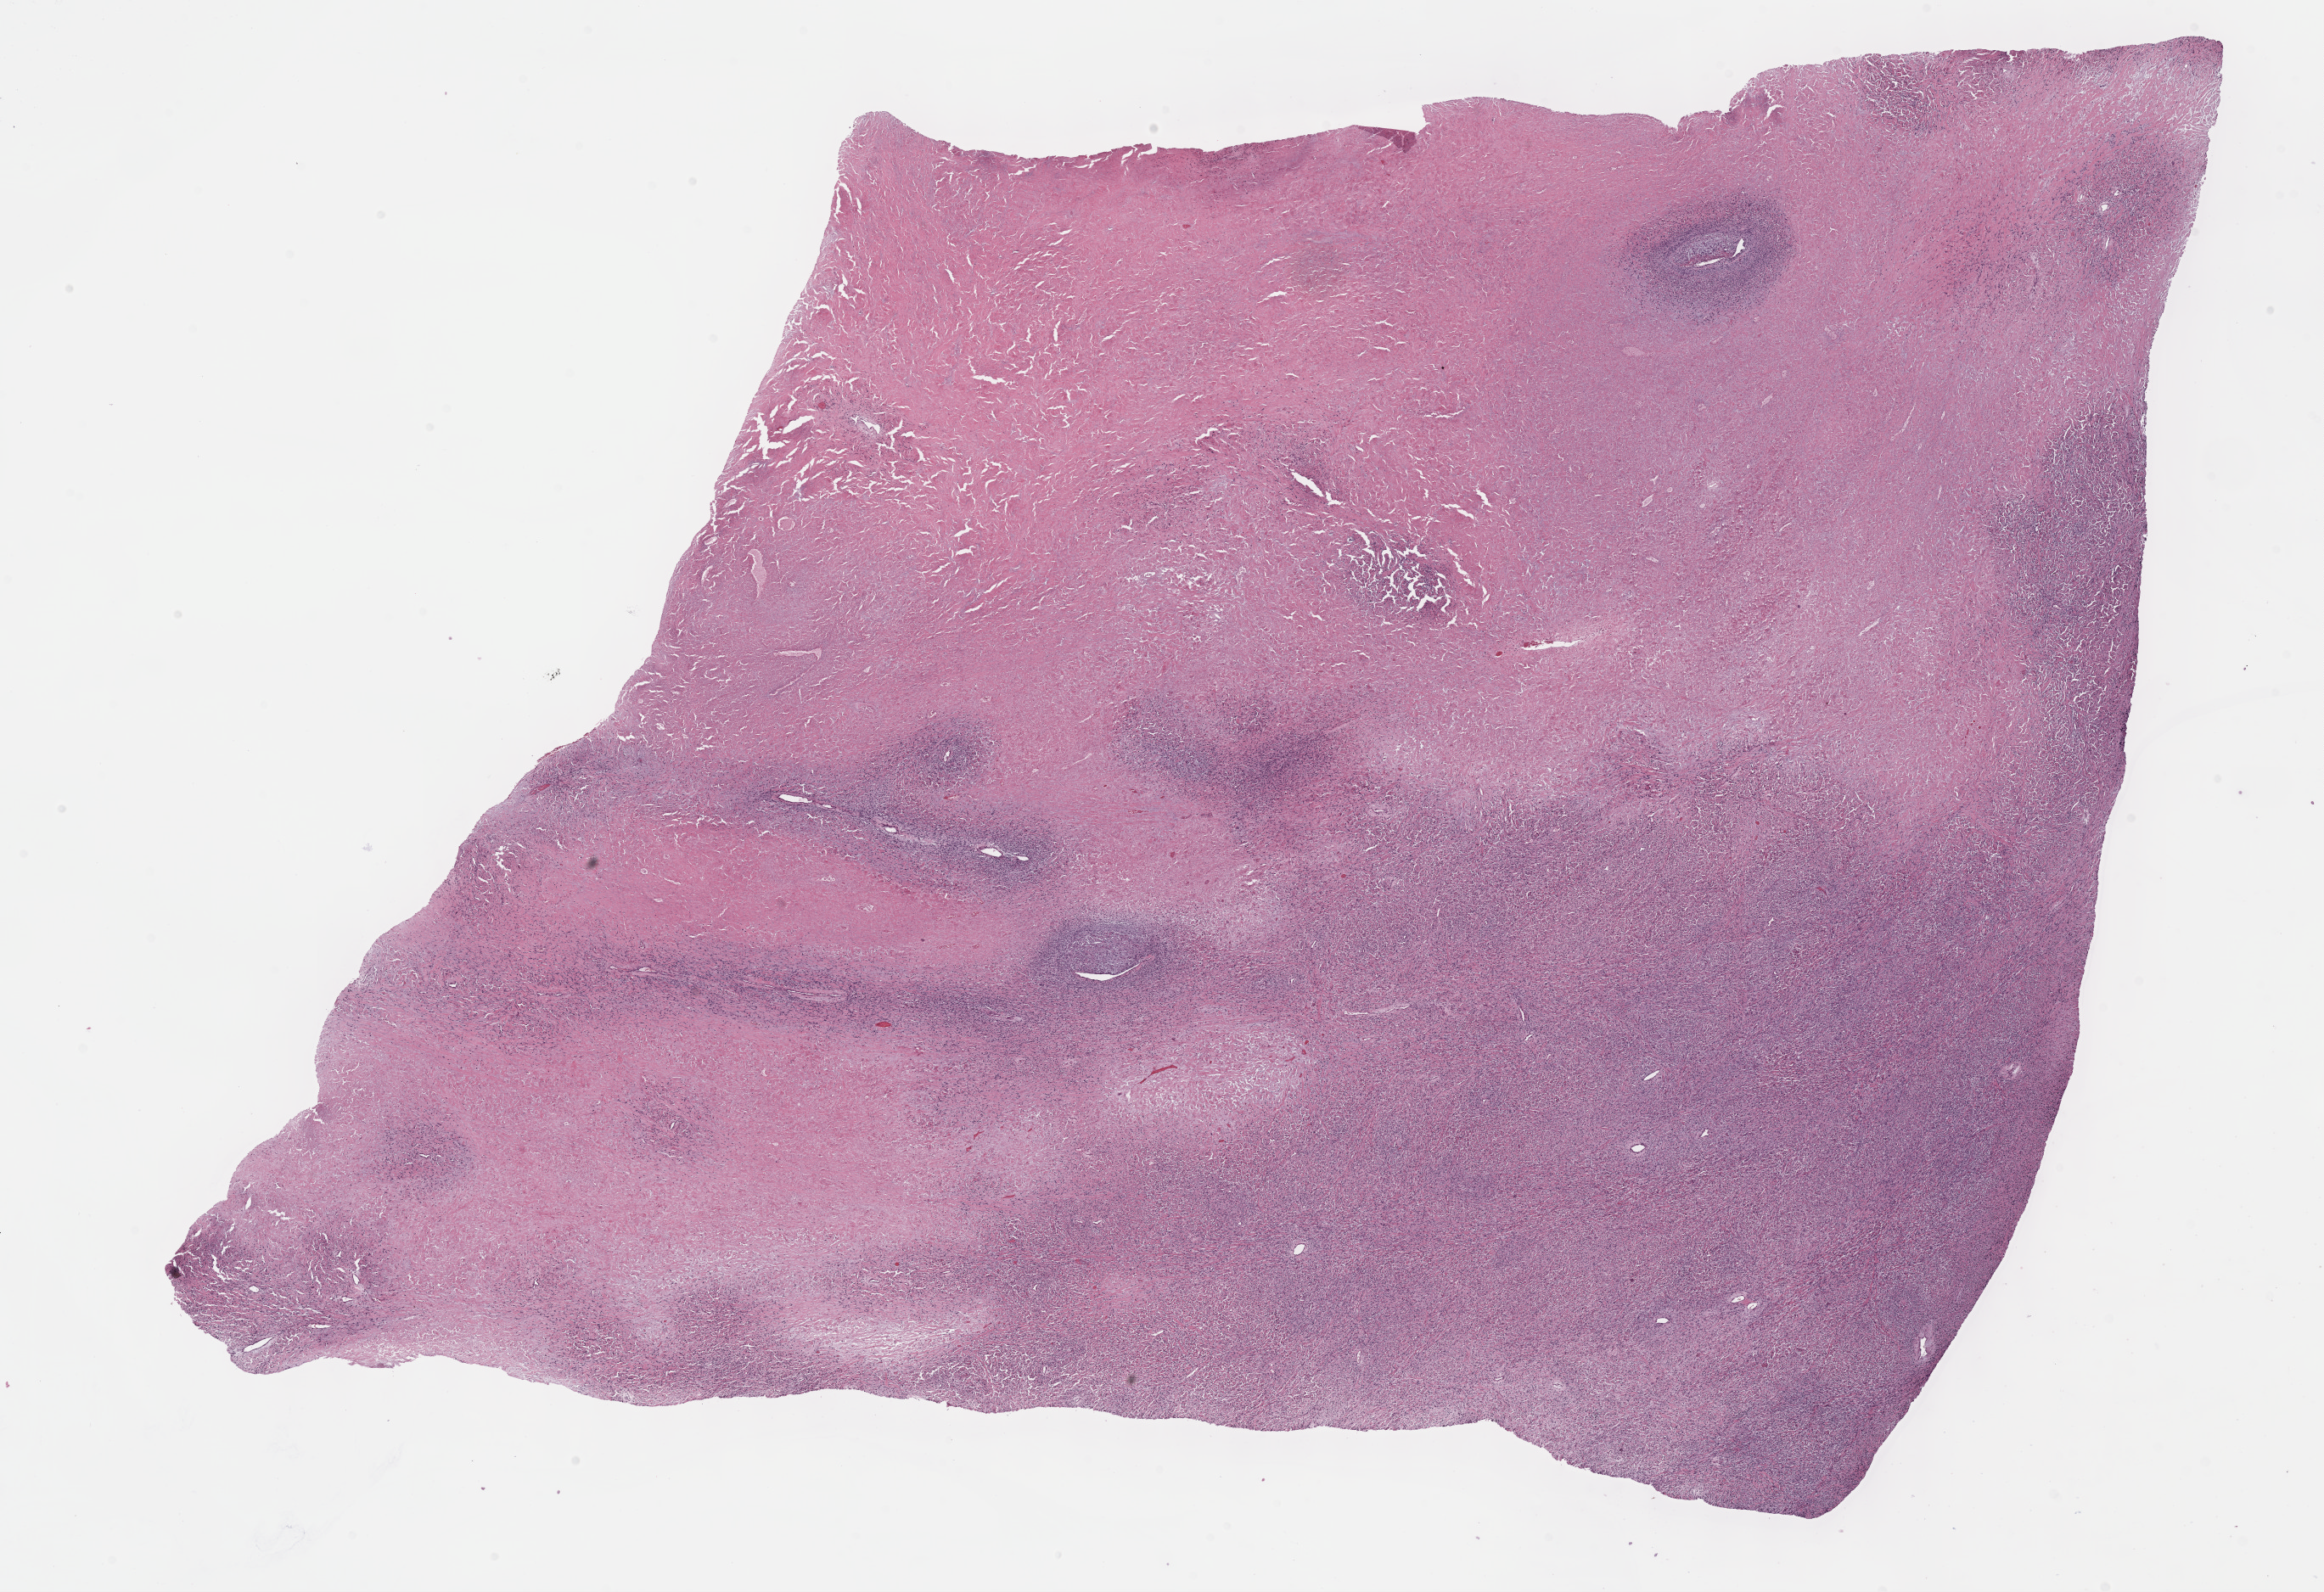
Whole-slide histology image, Hematoxylin and eosin (H&E) stained, whole scanned area (about 22.1 x 15.2 mm, acquisition: 40x scan) shown as a low-resolution overview. FFPE section. Sample: primary tumour, connective, subcutaneous and other soft tissues. Patient: female, age at initial diagnosis 20 years.
• histologic diagnosis: Malignant peripheral nerve sheath tumor (connective, subcutaneous and other soft tissues of lower limb and hip)